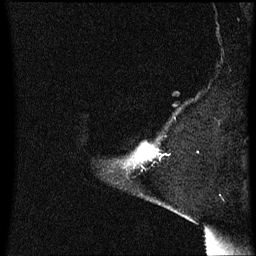
Breast MRI (dynamic contrast-enhanced), one sagittal slice; slice 54 of 60 in the series (ordered by position); dynamic contrast-enhanced series, image 2 of 3 at this slice position (ordered by acquisition); 1.5 T; TE 4.2 ms, TR 8.4 ms; 2 mm slice thickness; 256 × 256 image matrix, field of view 200 × 200 mm. Patient: female, 54 years. Case-level facts recorded for this patient, not image findings: setting: breast cancer imaged before/during neoadjuvant chemotherapy; receptor status: HR-positive, HER2-negative.
Annotated regions visible in this slice (semi-automatically segmented with operator editing):
- analysis volume of interest (the breast-tissue region the enhancement analysis was run in; not a lesion): bounding box <129,144,159,167> (left, top, right, bottom; pixels)
- tumour enhancement mask (voxels above the 70 % enhancement threshold inside the analysis volume of interest): <138,144,155,159>